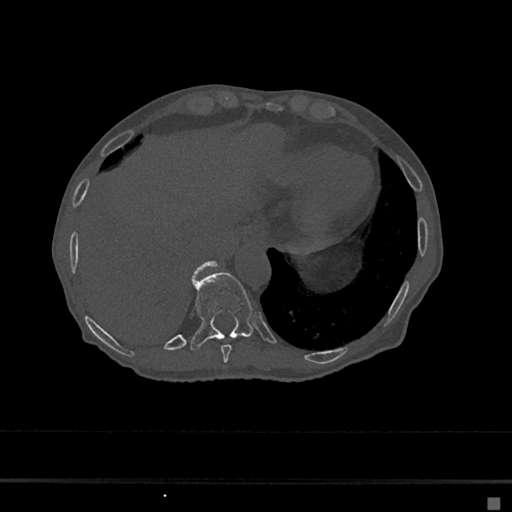
CT including the spine, one axial slice. Position 235 of 797 along the scan axis. 120 kVp. Bone window (W 1800 / L 400 HU). 0.5 mm slice thickness. 512 × 512 image matrix, field of view 360 × 360 mm. Female patient, age 68 years. From the clinical record (not read from this slice): primary cancer: renal.
Outlined on this slice (semi-automatically segmented with operator editing):
- T10 vertebra: bounding box (x1, y1, x2, y2) in pixels: (190, 272, 256, 350)
- T11 vertebra: (193, 261, 217, 278)
- T9 vertebra: (220, 345, 232, 363)